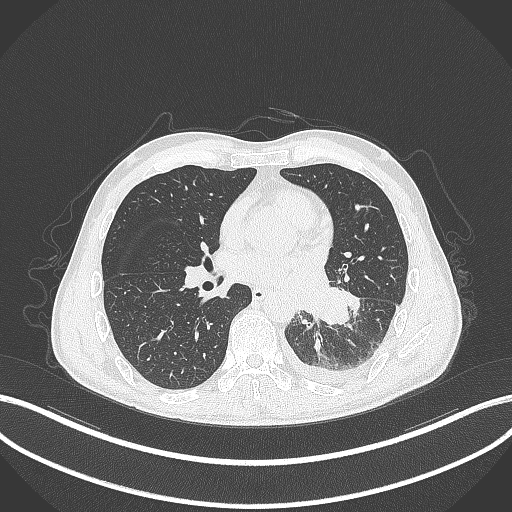
Chest CT, one axial slice; position 146 of 295 along the scan axis; lung window (W 1500 / L -600 HU); 512 × 512 image matrix, field of view 400 × 400 mm. Male patient, age 47 years. Case-level facts recorded for this patient, not image findings: clinical TNM (as recorded): T3 N1 M1c.
Structures marked on this image (rectangle marked by the reading radiologist):
- lung tumour (recorded histology: small cell carcinoma): box from (x=306, y=283) to (x=351, y=329) px